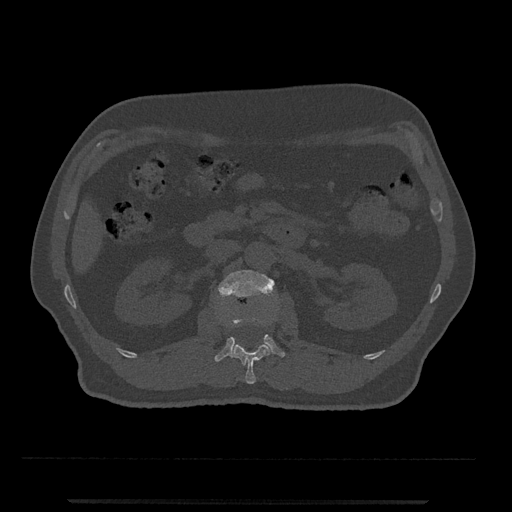
CT including the spine, one axial slice; position 301 of 797 along the scan axis; 120 kVp; bone window (W 1800 / L 400 HU); 0.5 mm slice thickness; 512 × 512 image matrix, field of view 419 × 419 mm. Male patient, age 63 years. Case-level facts recorded for this patient, not image findings: primary cancer: prostate.
Annotated regions visible in this slice (semi-automatic segmentation, software-assisted and operator-edited):
- L1 vertebra: bounding box [x1, y1, x2, y2] px = [231, 322, 270, 384]
- L2 vertebra: [214, 270, 285, 362]